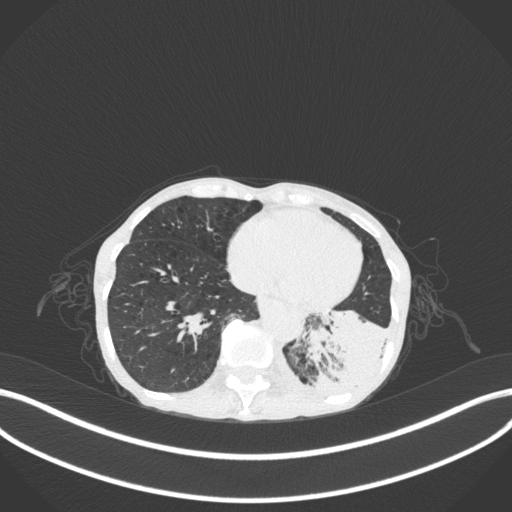
Chest CT, one axial slice; position 66 of 347 along the scan axis; reconstruction kernel B31f; lung window (W 1500 / L -600 HU); 1 mm slice thickness; 512 × 512 image matrix, field of view 400 × 400 mm. Female patient, age 70 years. Case-level facts recorded for this patient, not image findings: clinical TNM (as recorded): T3 N0 M0; histopathological grade: G3.
Annotated regions visible in this slice (bounding box drawn by a radiologist):
- lung tumour (recorded histology: small cell carcinoma): bounding box (x1, y1, x2, y2) in pixels: (301, 302, 392, 406)